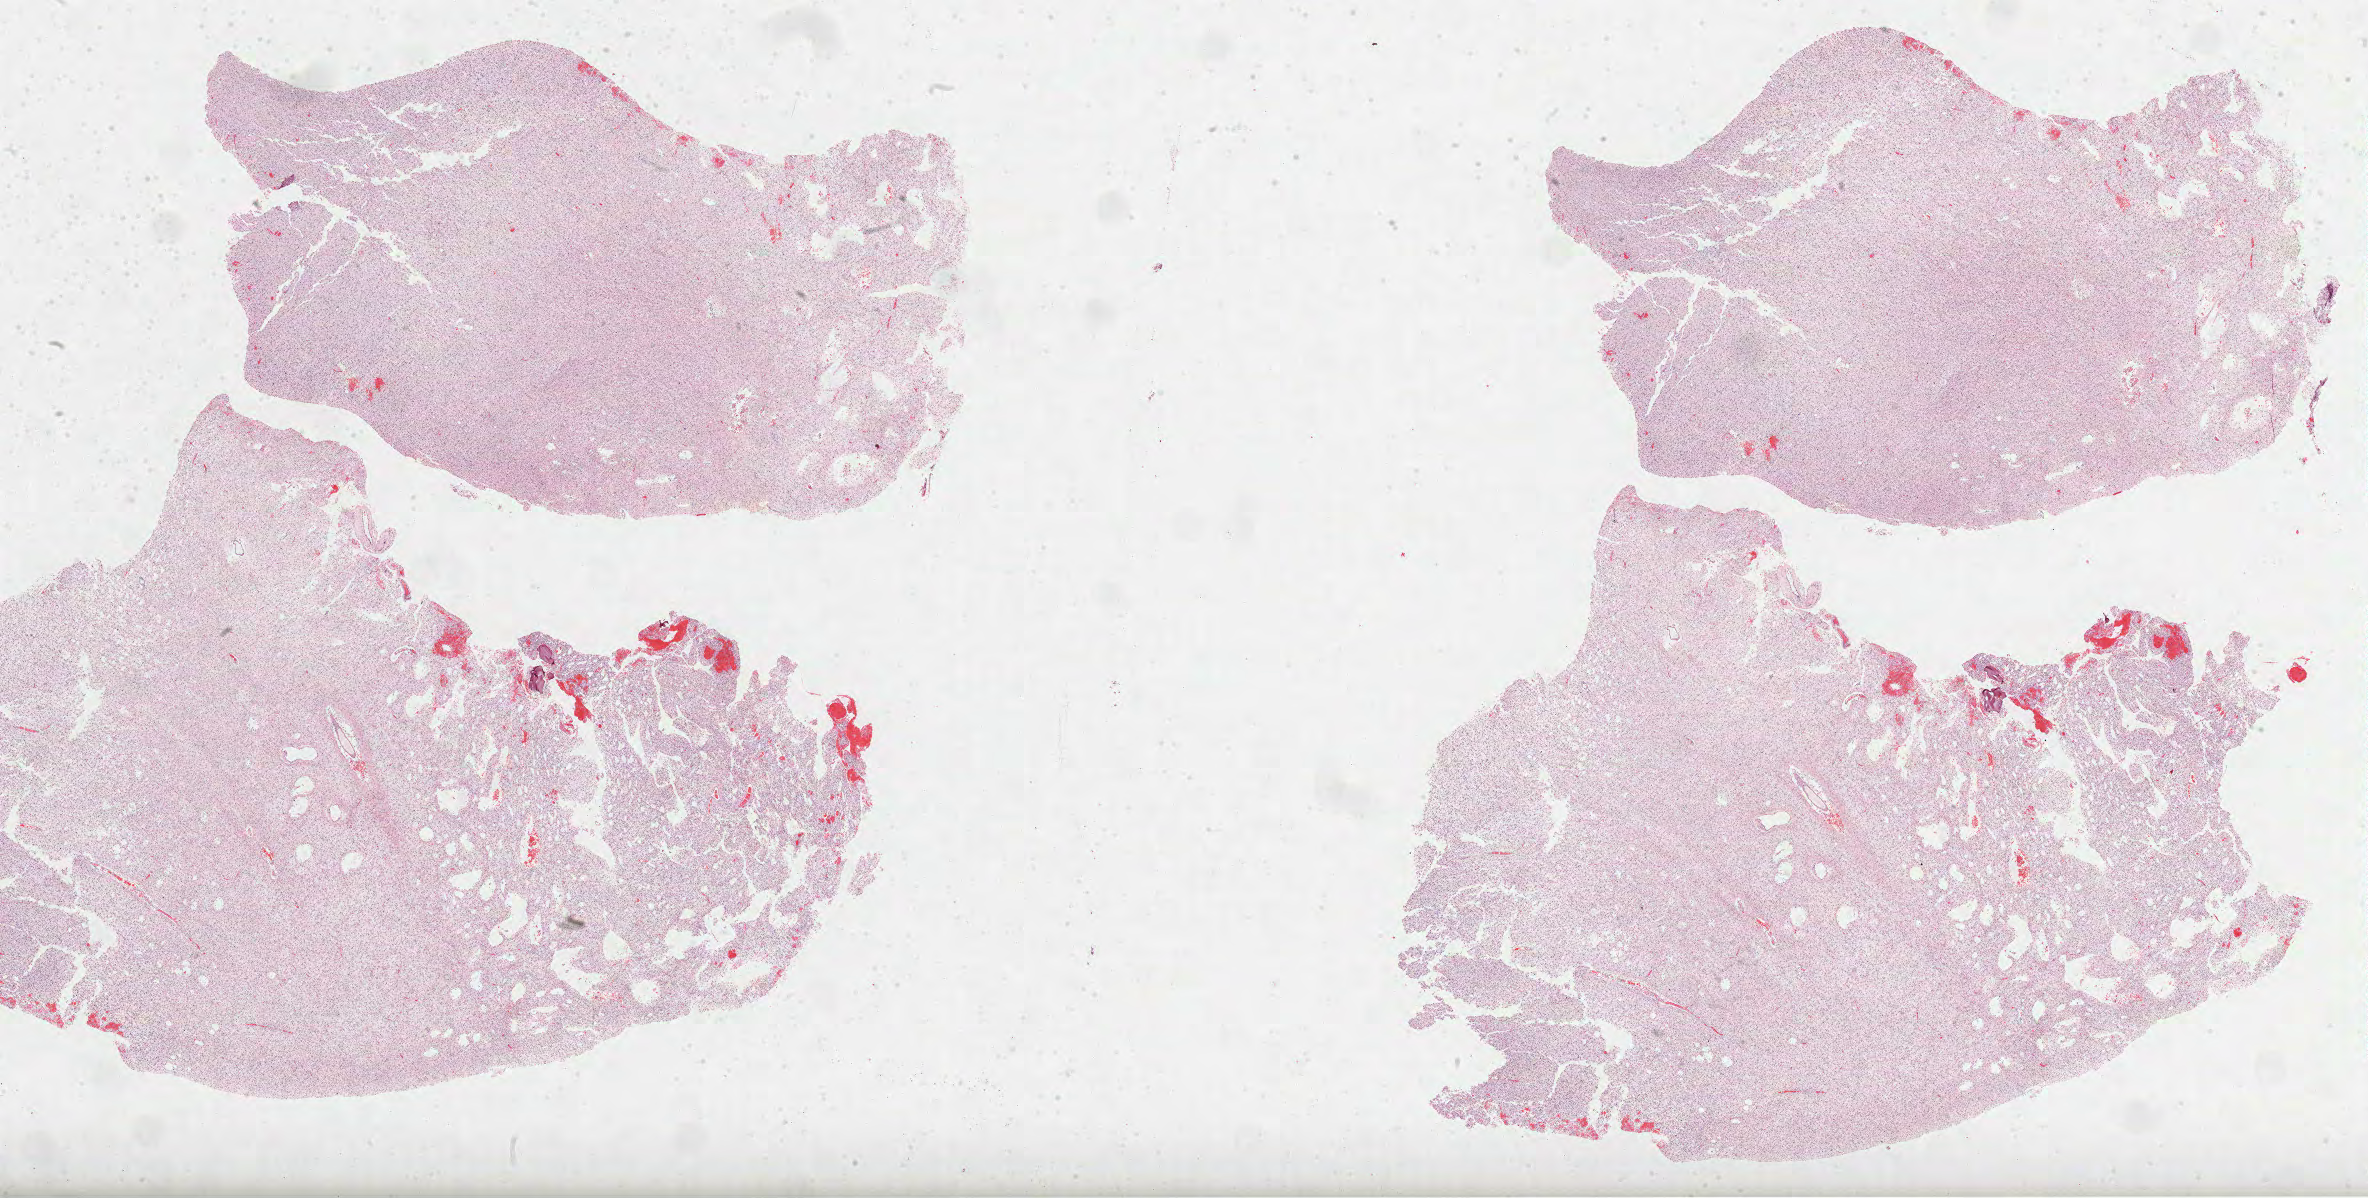
Whole-slide histology image, Hematoxylin and eosin (H&E) stained, whole scanned area (about 38.2 x 19.3 mm) shown as a low-resolution overview. FFPE section. Sample: primary tumour, brain. Female patient; age at initial diagnosis 23 years. Histologic grade: G2 (moderately differentiated).
• pathologic diagnosis: Astrocytoma, NOS